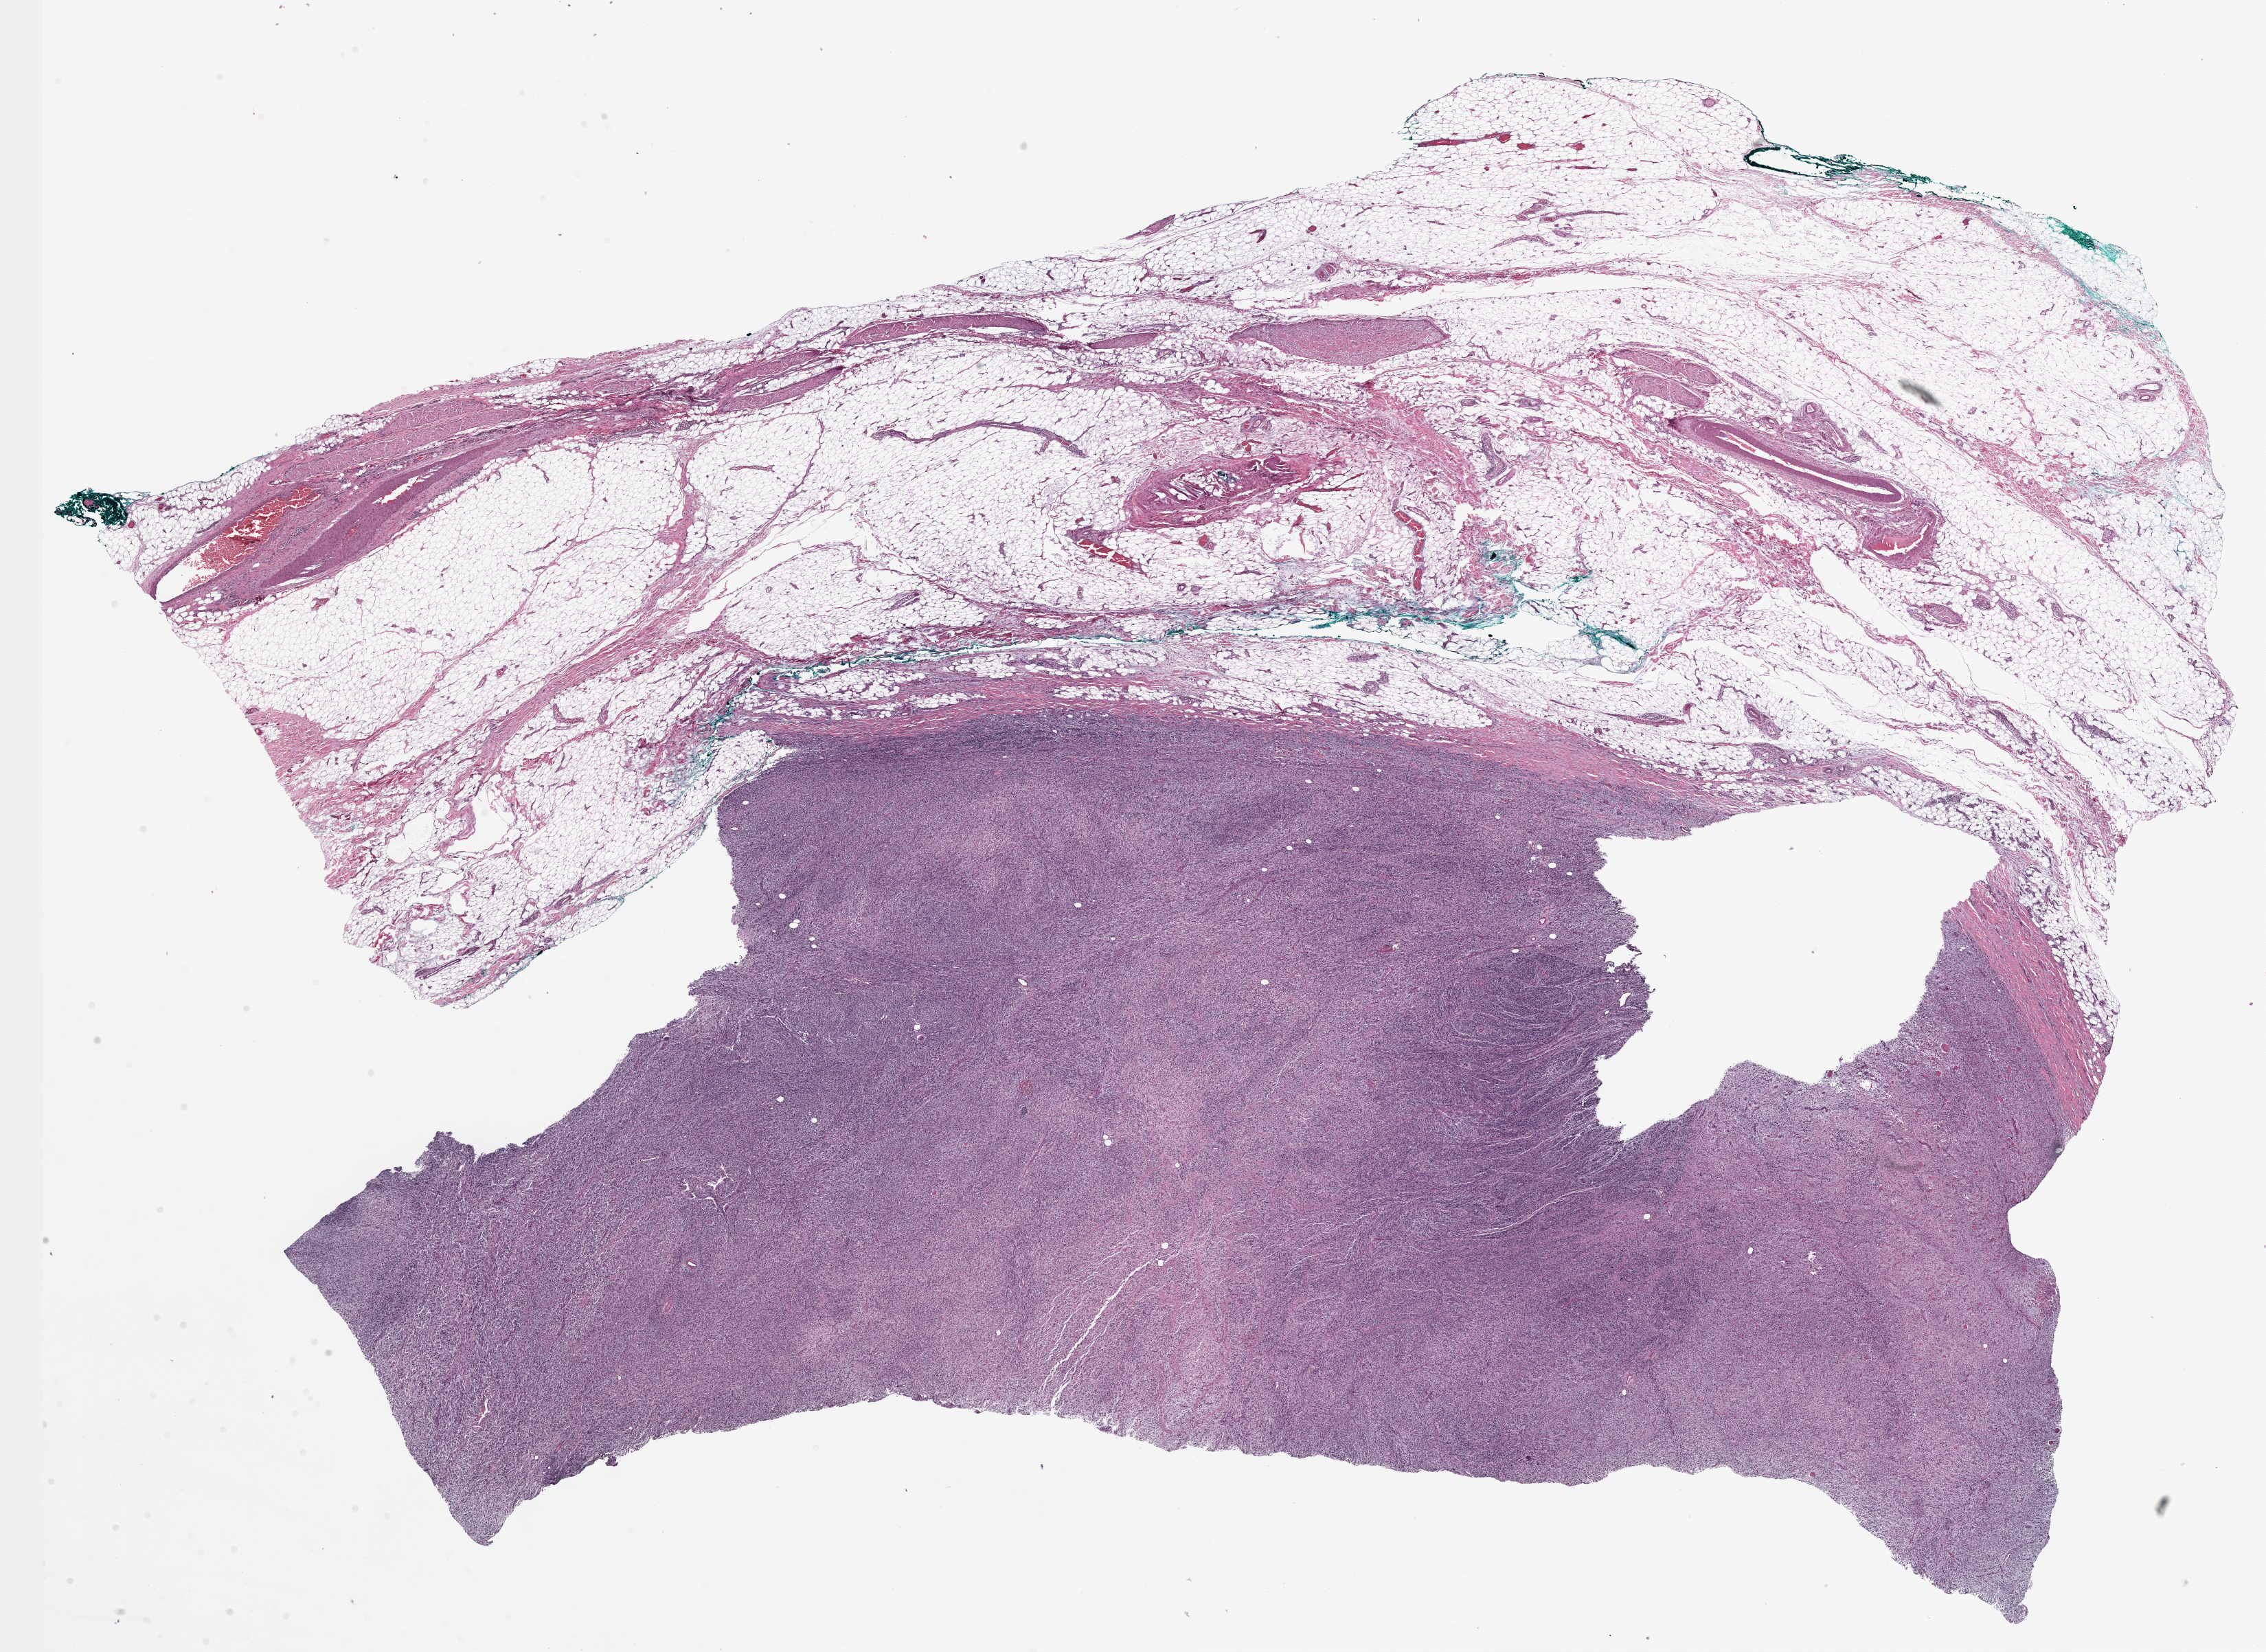
Whole-slide histology image, H&E-stained — whole scanned area (about 26.7 x 19.4 mm, slide scanned at 40x) shown as a low-resolution overview; formalin-fixed paraffin-embedded (FFPE) diagnostic section; primary tumour sample from the connective, subcutaneous and other soft tissues. Patient: female, age at initial diagnosis 34 years.
• histologic diagnosis: Malignant peripheral nerve sheath tumor